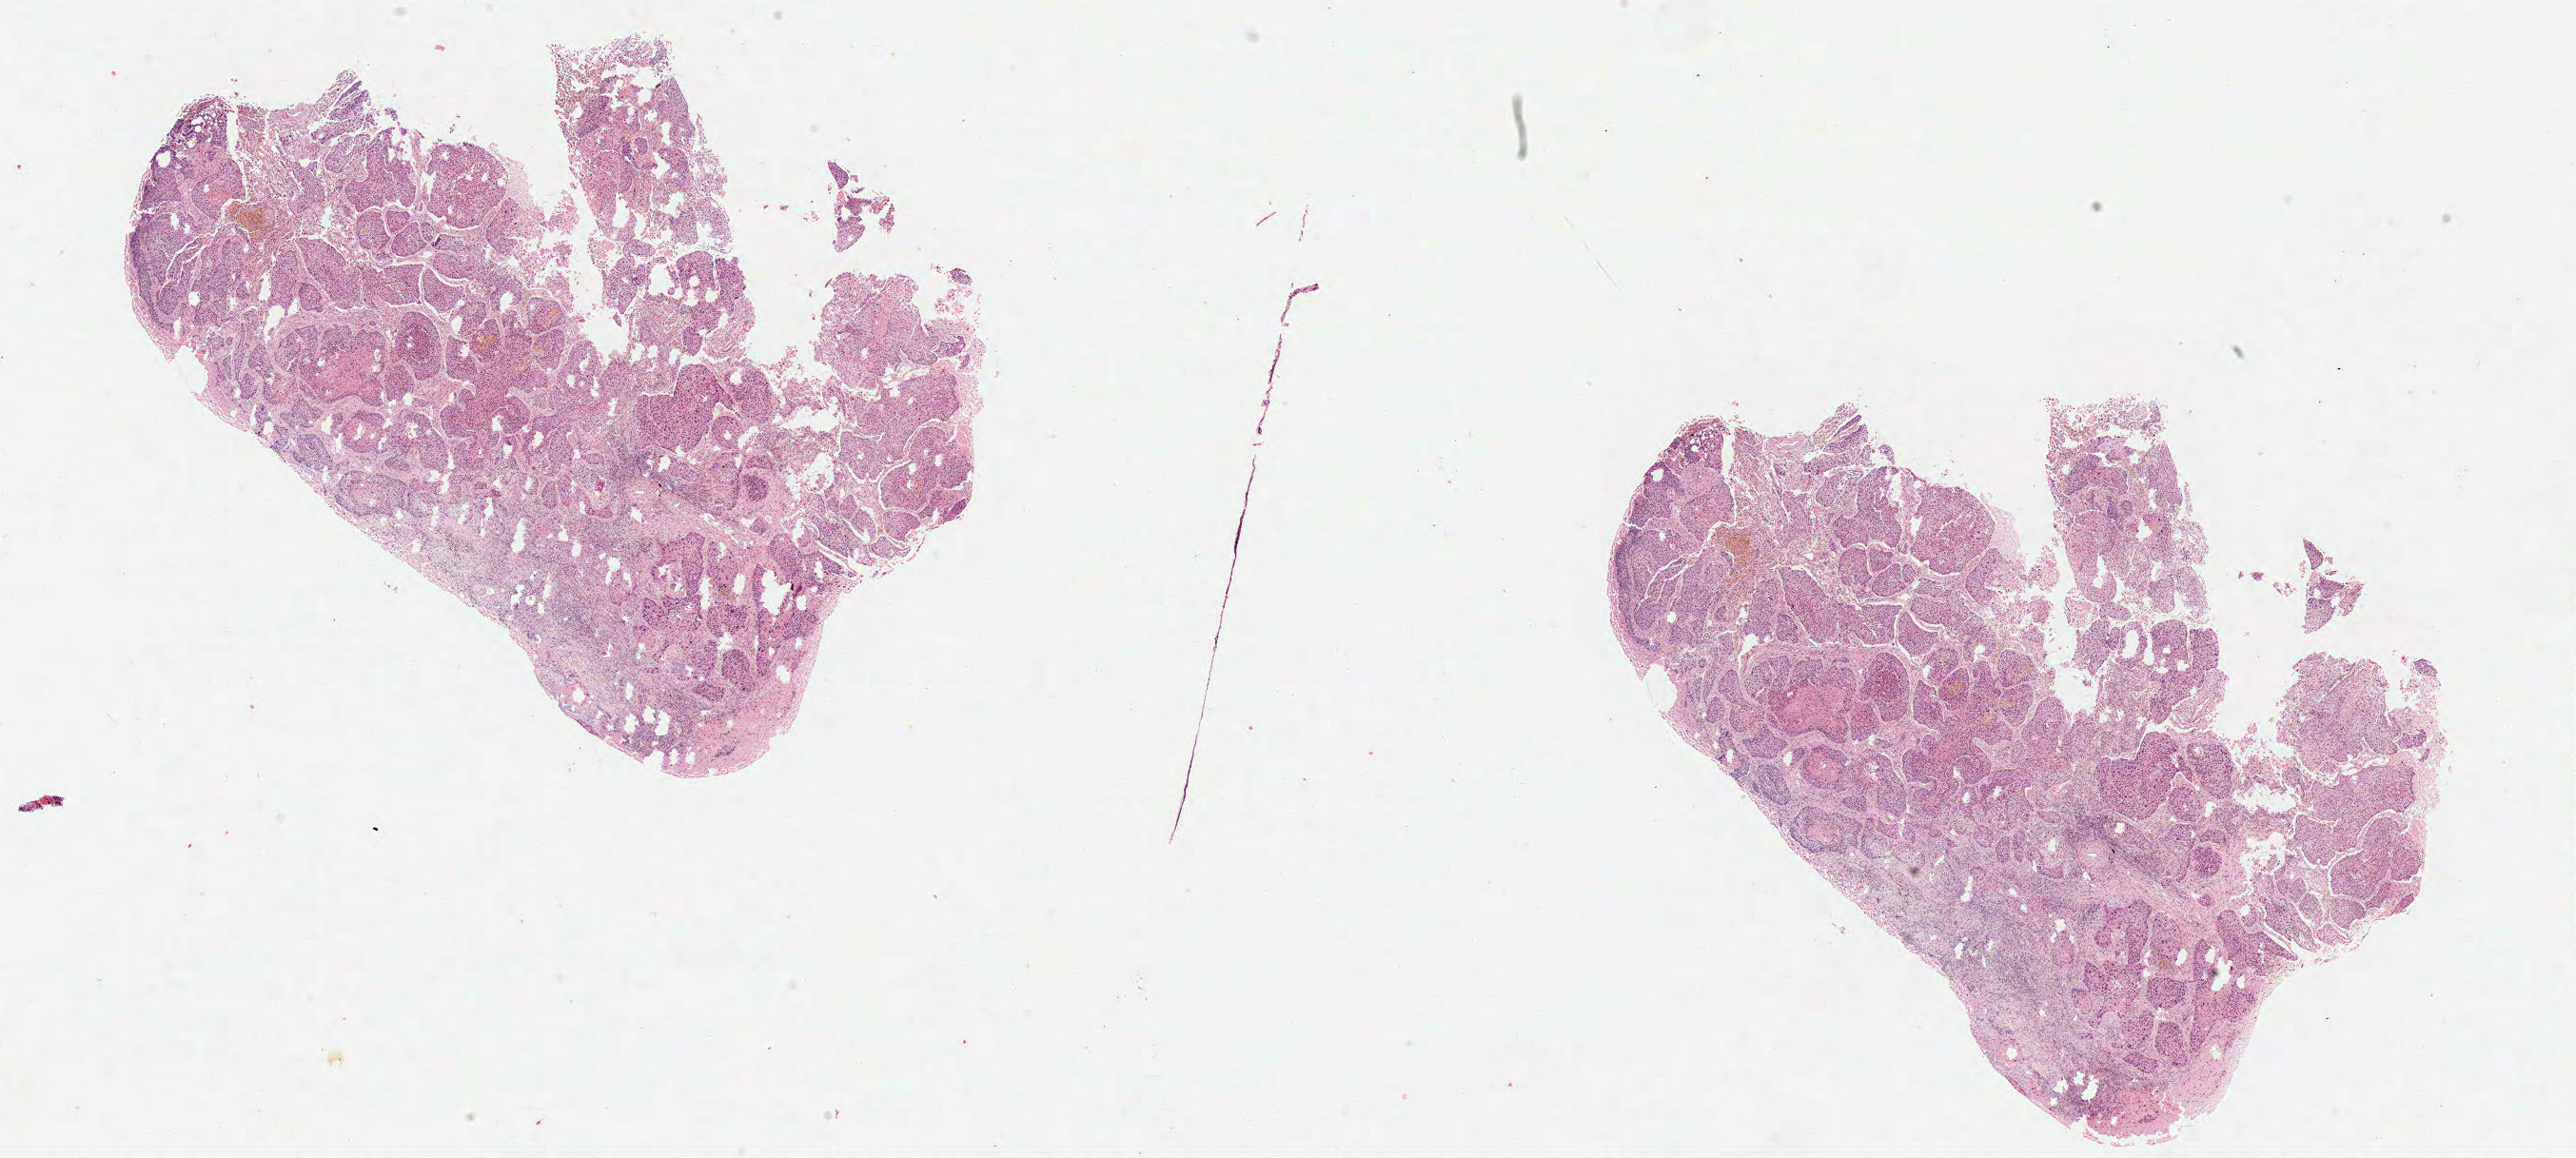
Whole-slide histology image, H&E — a low-resolution overview of the entire scanned area, about 21.3 x 9.6 mm (acquisition: 40x scan). Frozen section from the top of the tissue portion. Sample: primary tumour, lung. Male, age 69 years at initial diagnosis. Slide review estimates, as recorded: tumour cells 85%, tumour nuclei 80%, normal cells 0%, stromal cells 10%, necrosis 5%.
AJCC pathologic stage: IIB. Diagnosis: Squamous cell carcinoma, NOS (middle lobe, lung).